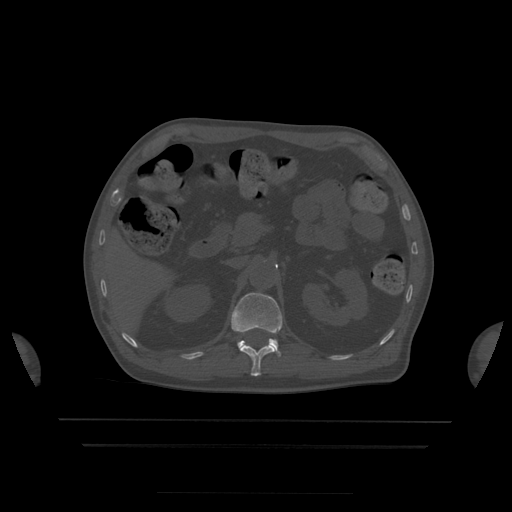
CT including the spine, one axial slice. Position 183 of 522 along the scan axis. Bone window (W 1800 / L 400 HU). 1.25 mm slice thickness. 512 × 512 image matrix. Patient age 68 years. Case-level facts recorded for this patient, not image findings: primary cancer: urothelial.
Outlined on this slice (semi-automatically segmented with operator editing):
- L1 vertebra: box from (x=232, y=293) to (x=283, y=357) px
- T12 vertebra: (x=240, y=344)–(x=276, y=377)